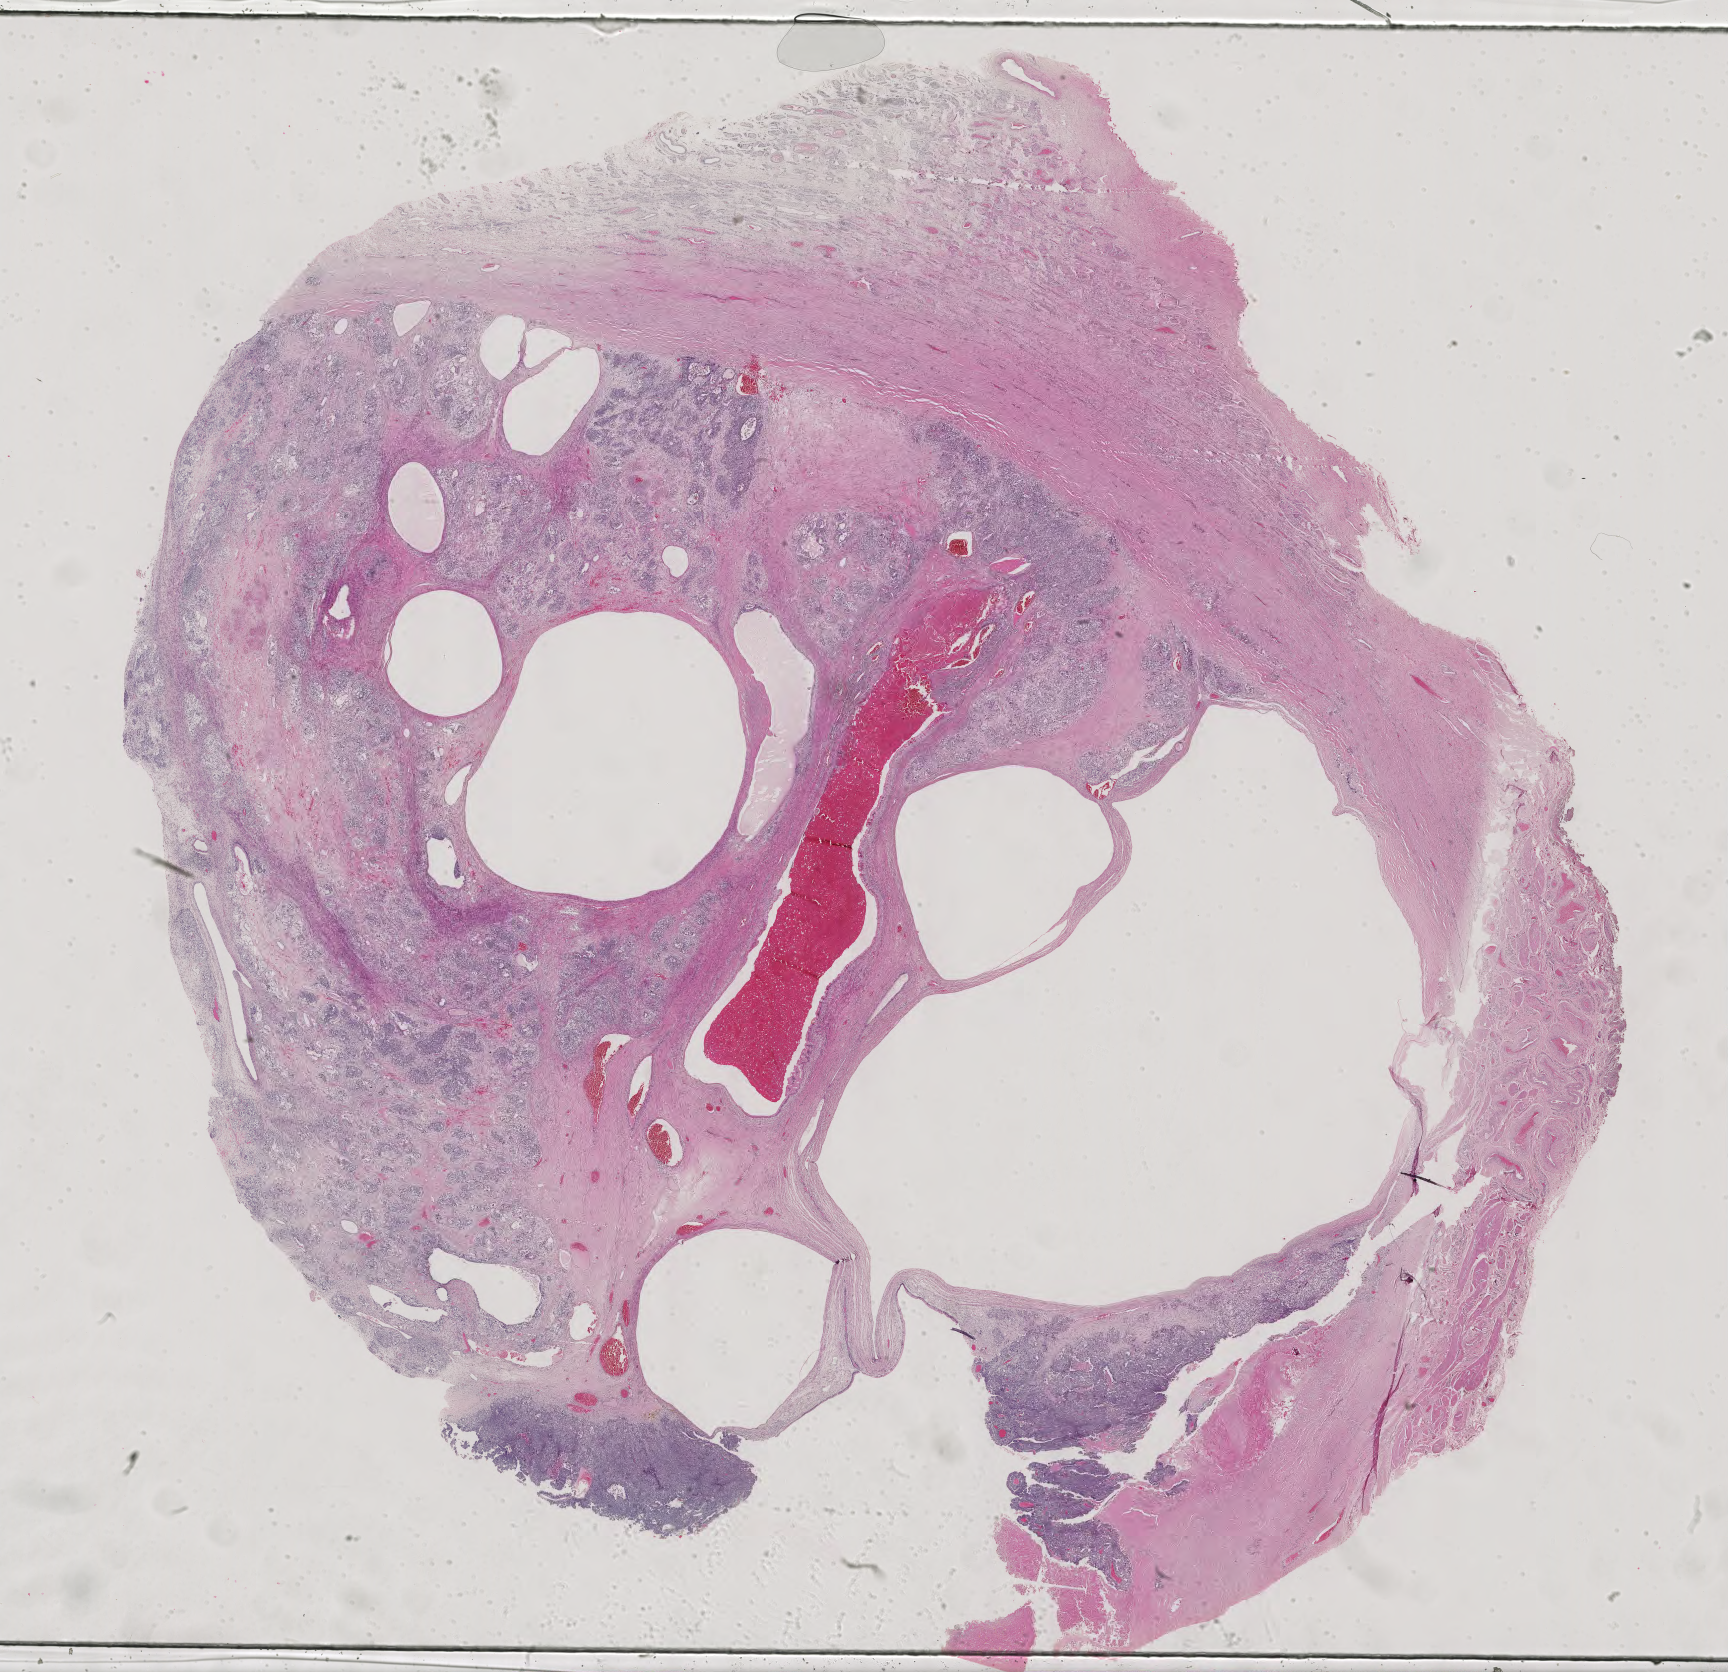
Whole-slide histology image, Hematoxylin and eosin (H&E) stained — shown as a low-resolution overview of the whole scanned area (about 25.2 x 24.4 mm, slide scanned at 40x), formalin-fixed paraffin-embedded (FFPE) diagnostic section, primary tumour sample from the testis. Male patient; age at initial diagnosis 25 years.
Laterality: left. Histologic diagnosis: Seminoma, NOS. AJCC pathologic stage: IIIB (6th edition).